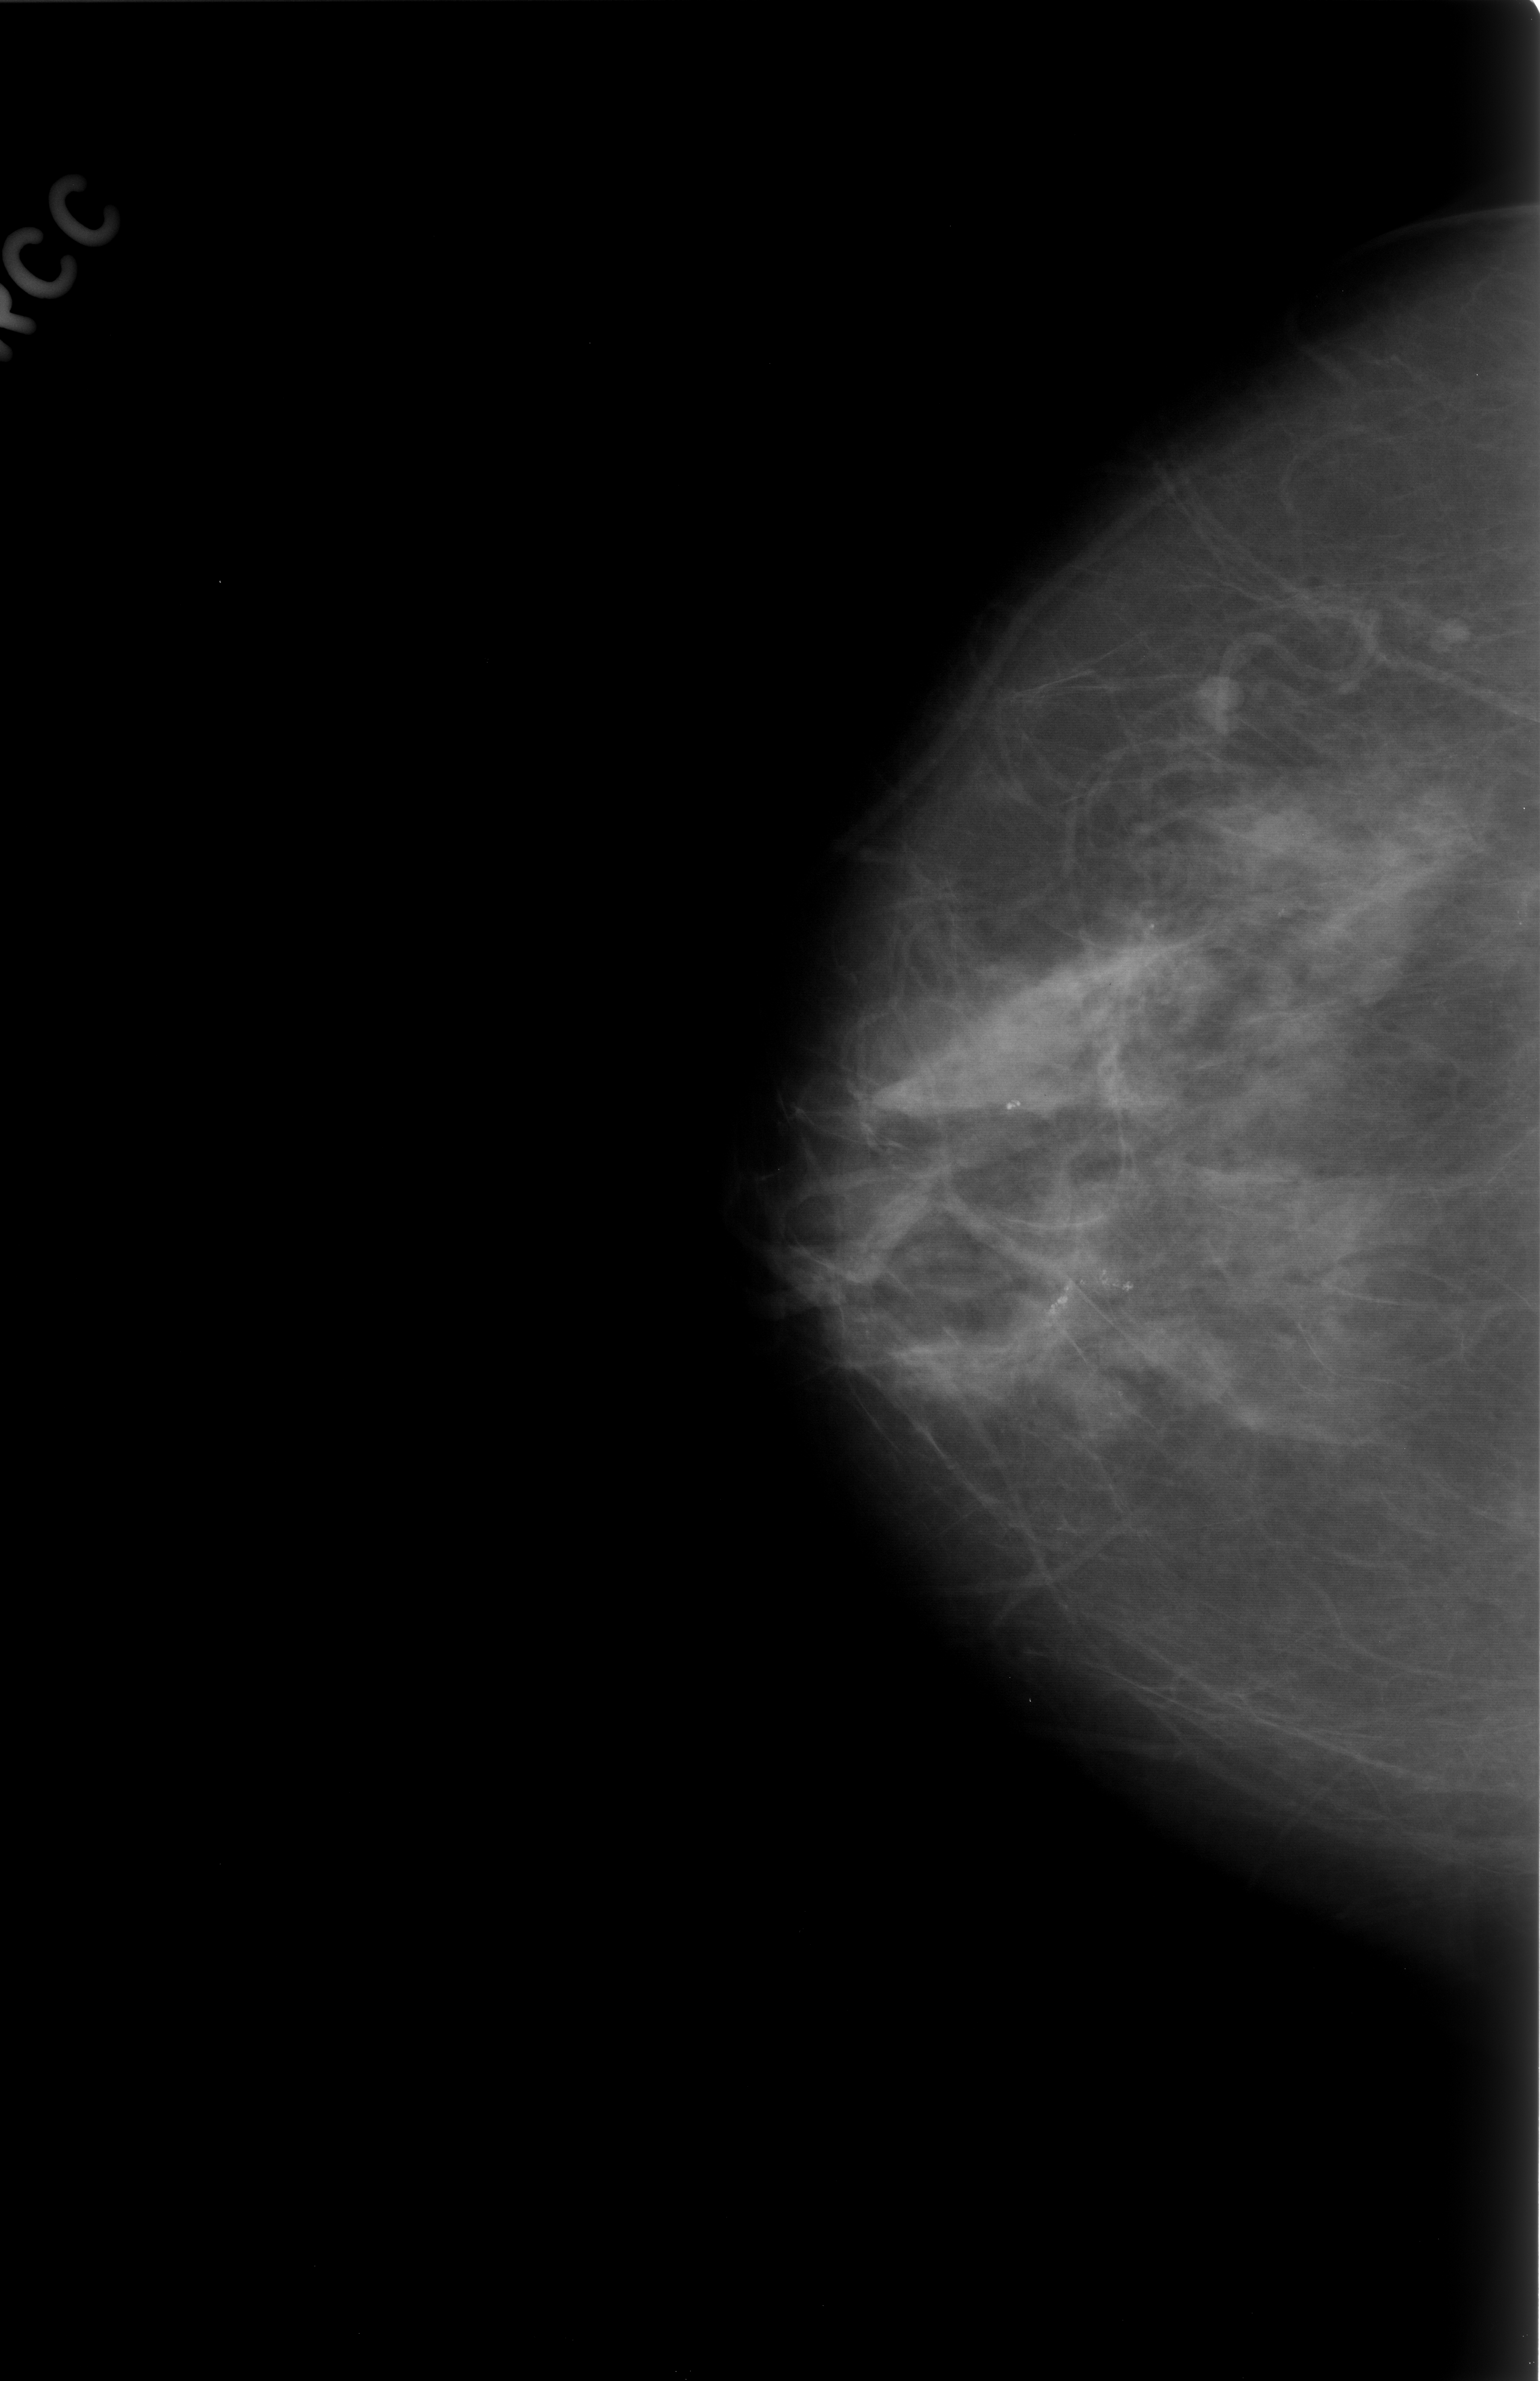
Digitized screen-film mammogram. Right breast. CC view. BI-RADS breast density category 2 (scale 1–4). 1540 × 2381 image matrix.
Marked abnormalities (boxes around the expert regions of interest):
- Finding 1 of 2: calcifications, morphology pleomorphic, distribution clustered; BI-RADS assessment category 3; pathology (as recorded): benign: bounding box (x1, y1, x2, y2) in pixels: (970, 1056, 1067, 1170)
- Finding 2 of 2: calcifications, morphology pleomorphic, distribution clustered; BI-RADS assessment category 4; pathology (as recorded): benign: (1003, 1185, 1183, 1352)